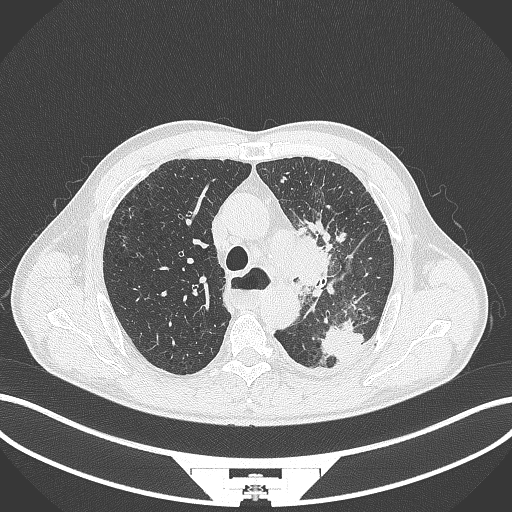
Chest CT, one axial slice; slice 277 of 411 in the series (ordered by position); 120 kVp; lung window (W 1500 / L -600 HU); 1 mm slice thickness; 512 × 512 image matrix, field of view 400 × 400 mm. Male patient, age 57 years. From the clinical record (not read from this slice): clinical TNM (as recorded): T2a N1 M0.
Annotated regions visible in this slice (bounding box drawn by a radiologist):
- lung tumour (recorded histology: squamous cell carcinoma): bounding box (x1, y1, x2, y2) in pixels: (288, 232, 331, 289)